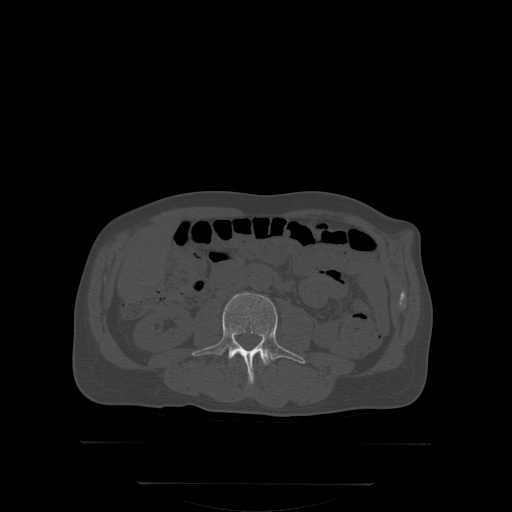
CT including the spine, one axial slice. Bone window (W 1800 / L 400 HU). 512 × 512 image matrix, field of view 500 × 500 mm. Male patient, age 58 years. From the clinical record (not read from this slice): primary cancer: prostate; vertebrae with lytic lesions (as recorded): L1.
Structures marked on this image (semi-automatically segmented with operator editing):
- L2 vertebra: bounding box (x1, y1, x2, y2) in pixels: (259, 354, 264, 362)
- L3 vertebra: (194, 292, 305, 386)